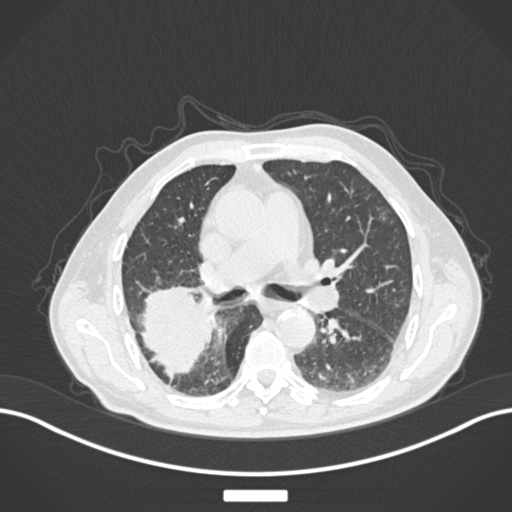
Chest CT, one axial slice. Slice 101 of 201 in the series (ordered by position). Reconstruction kernel B30f. 120 kVp. Lung window (W 1500 / L -600 HU). 512 × 512 image matrix. Patient: male, 72 years. From the clinical record (not read from this slice): clinical TNM (as recorded): T3 N2 M0.
Annotated regions visible in this slice (bounding box drawn by a radiologist):
- lung tumour (recorded histology: adenocarcinoma): box from (x=137, y=282) to (x=213, y=380) px